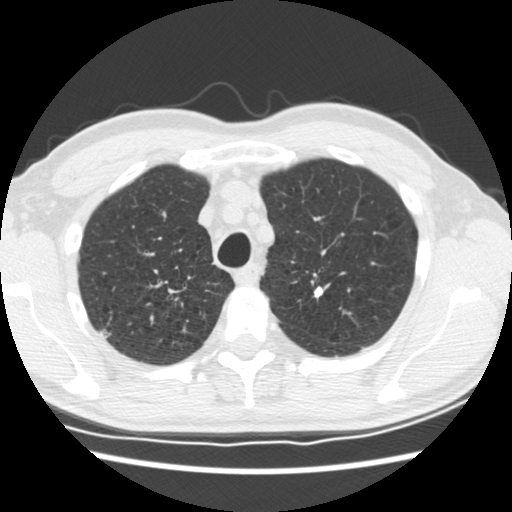
Low-dose screening chest CT, one axial slice. Position 144 of 183 along the scan axis. Lung window (W 1500 / L -600 HU). 512 × 512 image matrix, field of view 339 × 339 mm.
Structures marked on this image (manually delineated by an expert):
- lesion 2 (tumor, upper lobe of right lung): bounding box <99,328,111,338> (left, top, right, bottom; pixels)